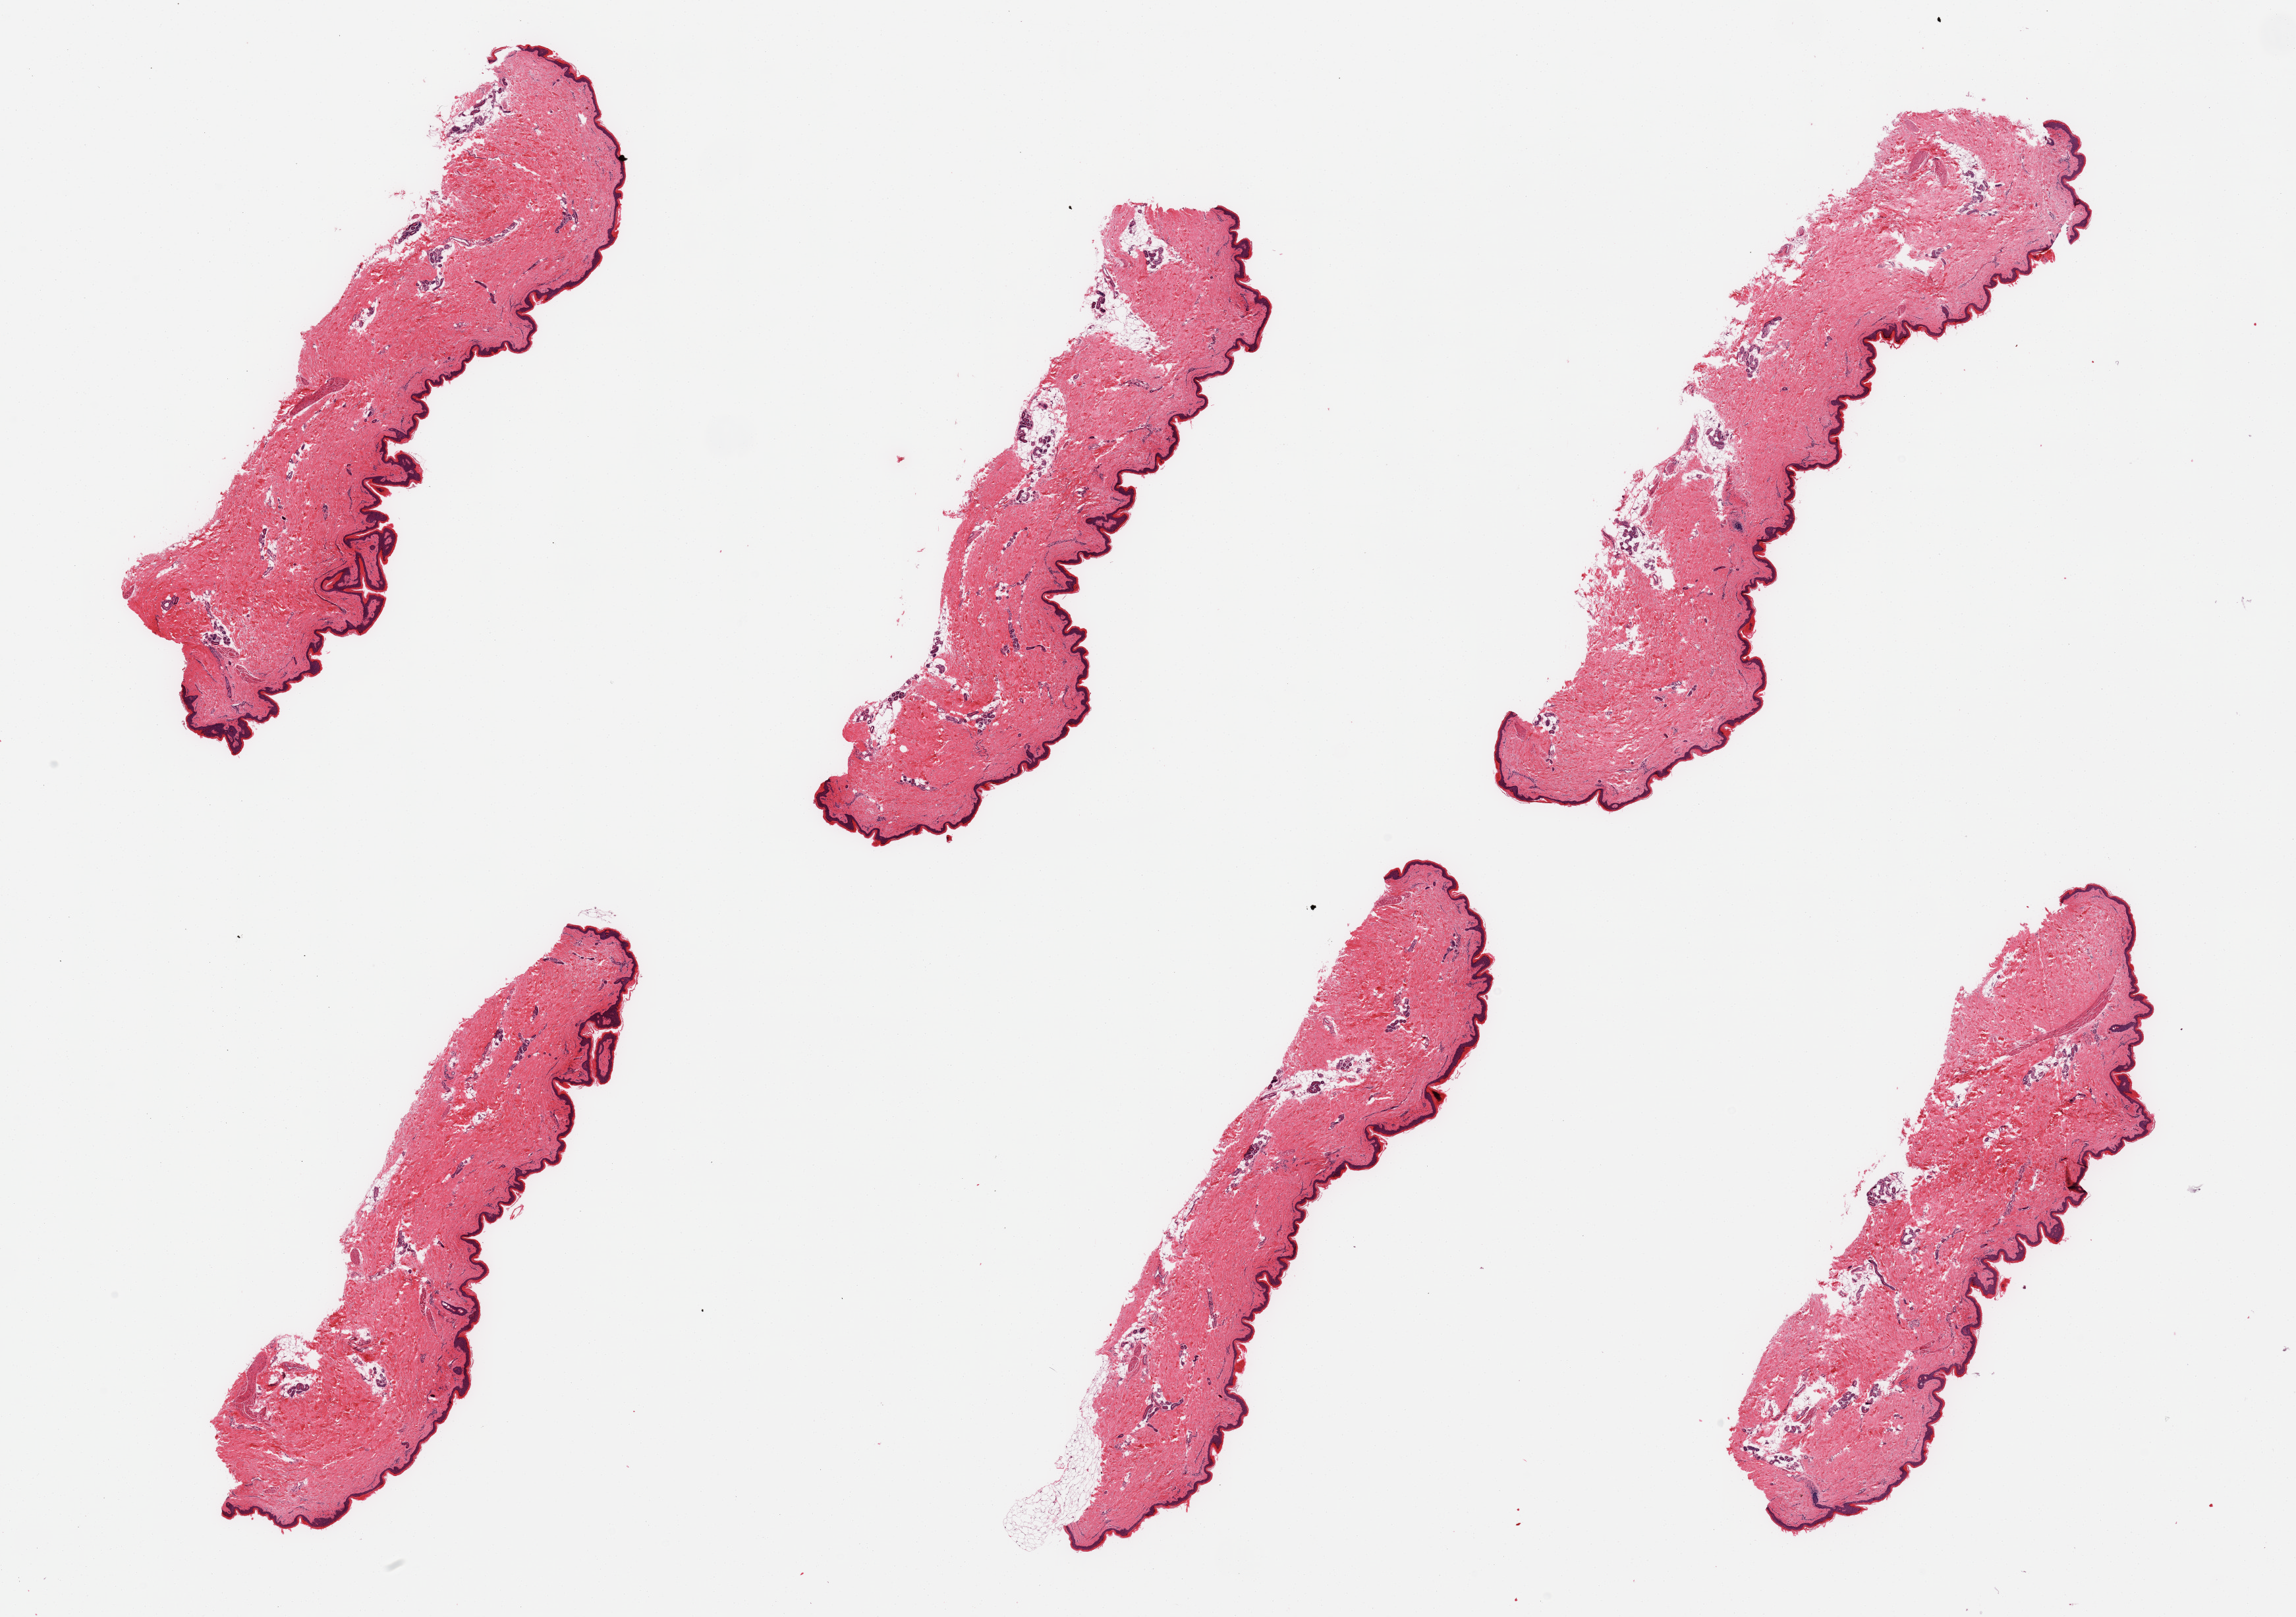
Digitized H&E-stained section, brightfield, a low-resolution overview of the entire scanned area, about 27.6 x 19.4 mm (from a 20x scan). PAXgene-fixed, paraffin-embedded tissue. Sampled site (target tissue): skin of lower leg. Donor tissue sample. Donor sex: female.
Pathologist's review note for this sample: 6 pieces; ~36 microns thick epidermis; ~10 to 15% internal fat (periadnexal).